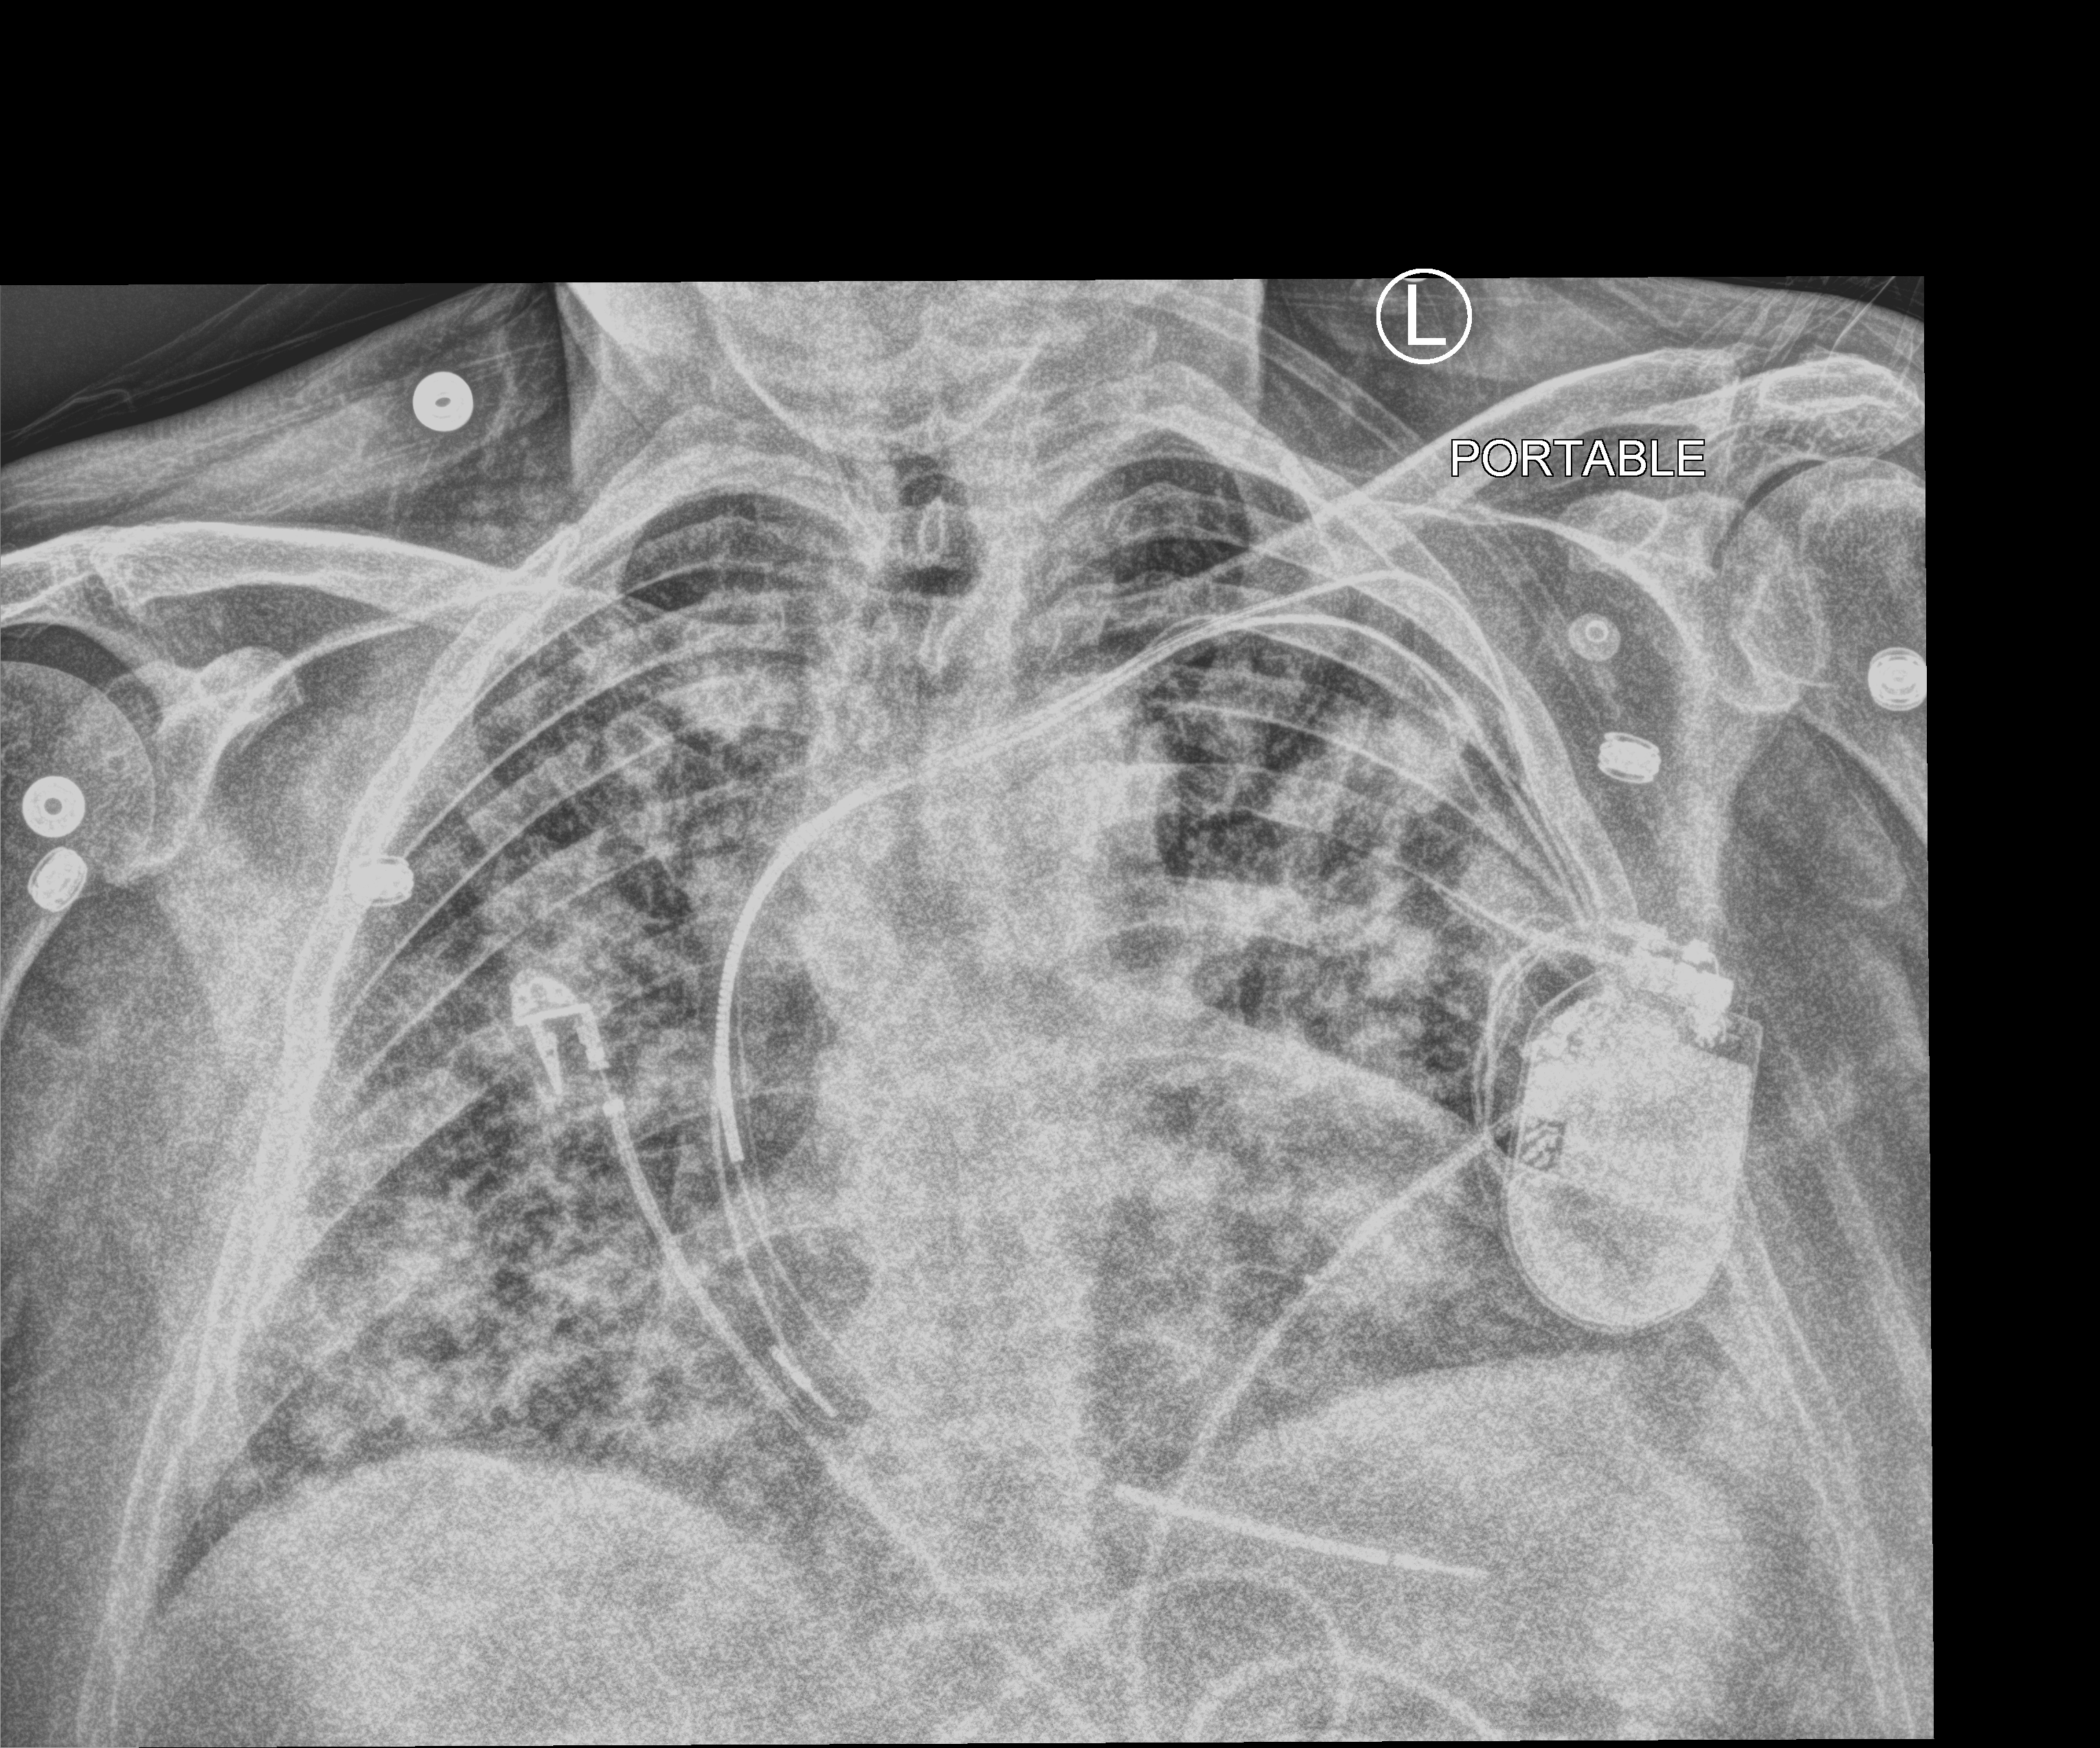
Bedside chest radiograph (computed radiography). Patient hospitalised with COVID-19; male, aged 60–74 years.
Hospital-stay facts (about this admission, not read from this image; timing relative to this image not recorded):
- admitted to intensive care during this hospital stay: no